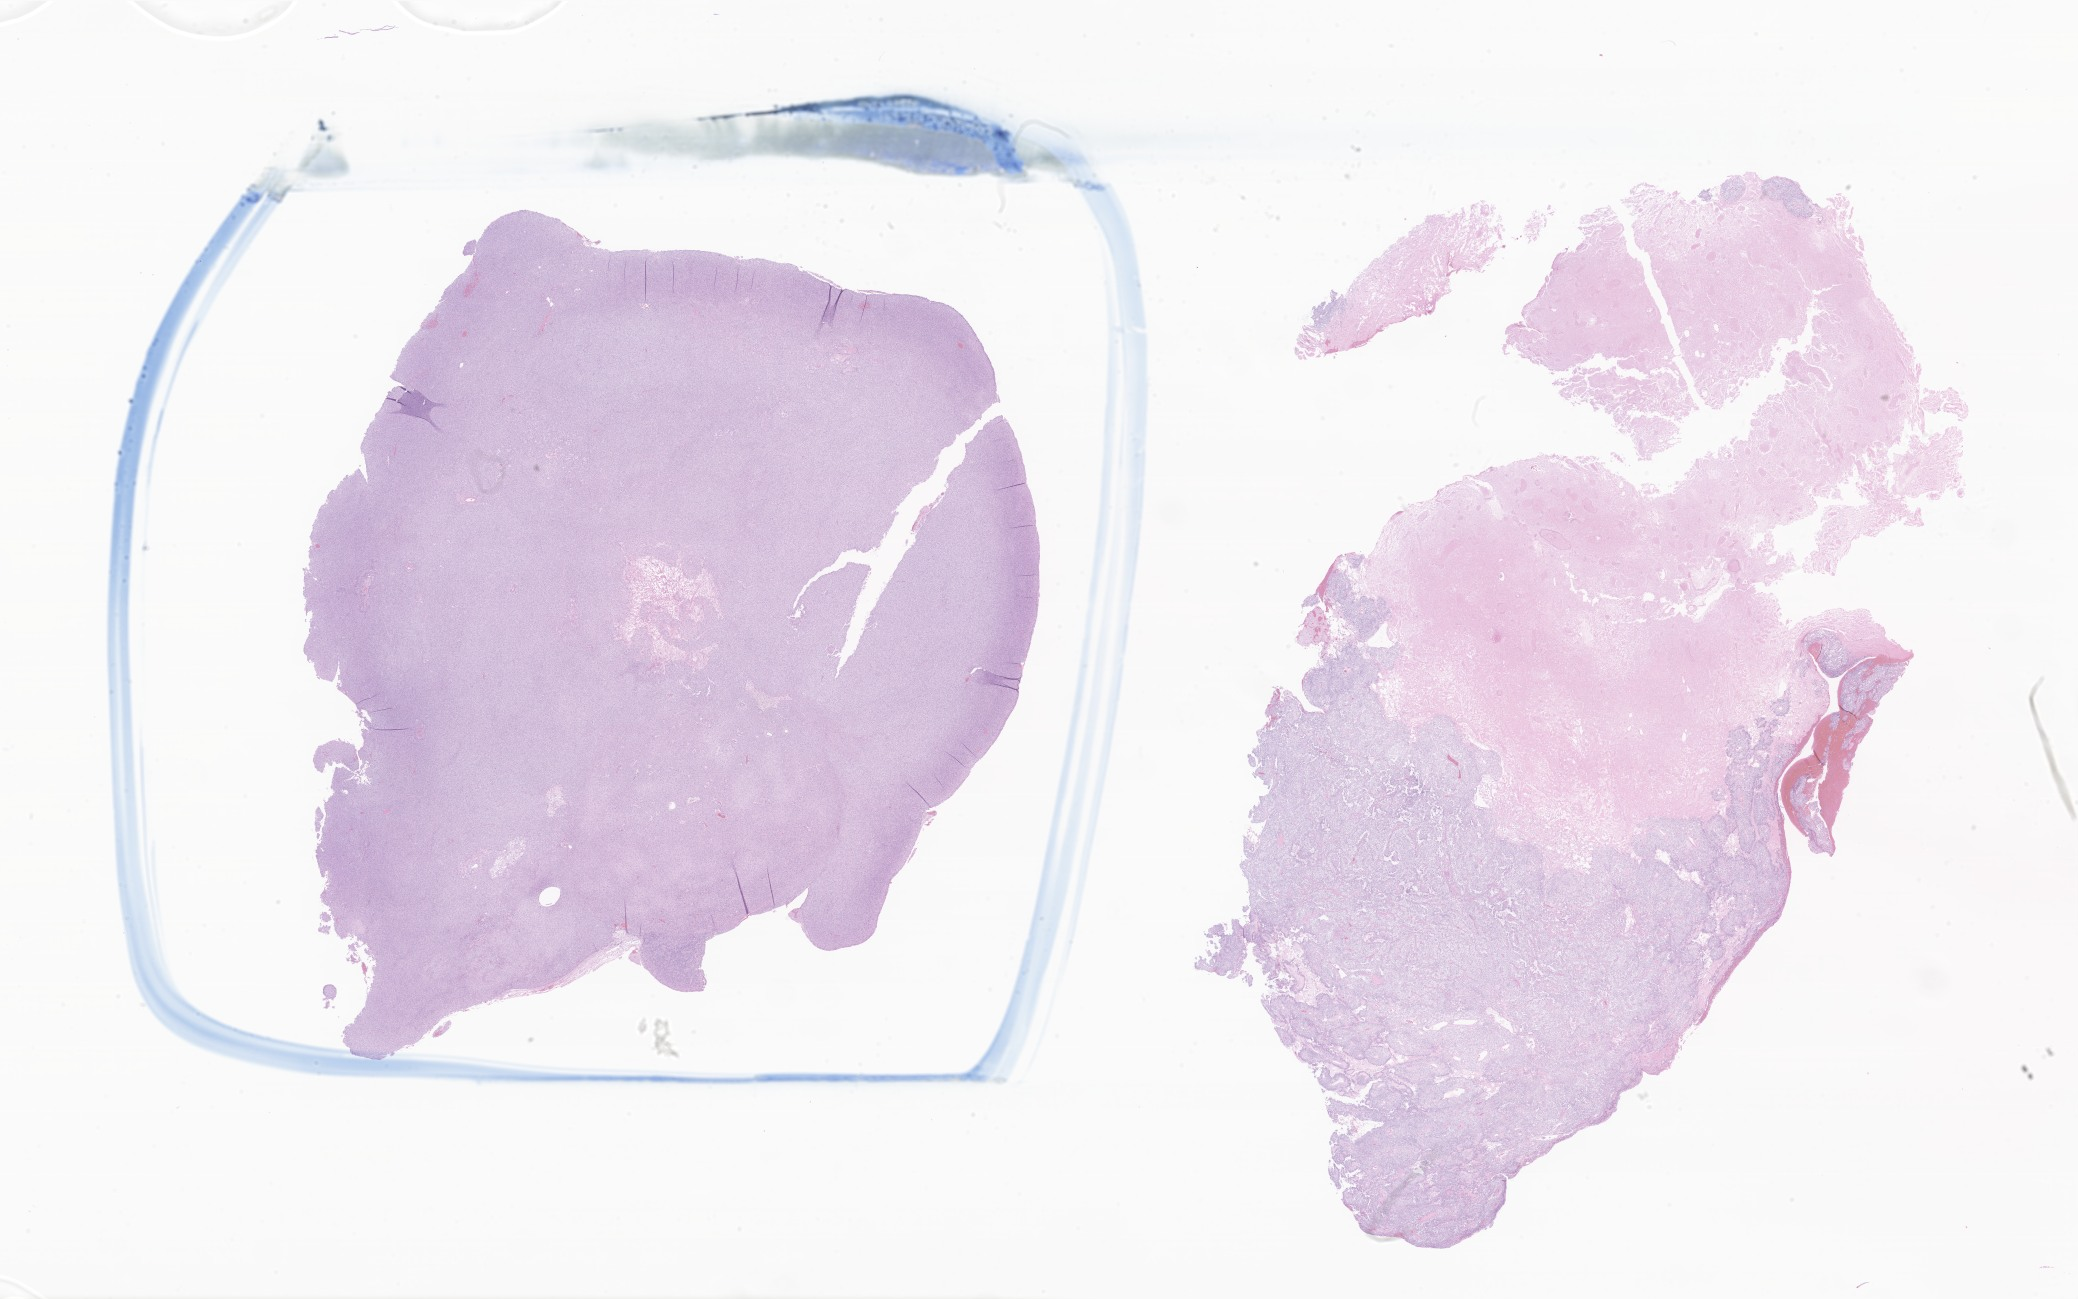
Whole-slide image, H&E stain of tumor tissue from the brain, shown as a low-resolution overview of the whole scanned area (about 35.0 x 21.9 mm); formalin-fixed, paraffin-embedded (FFPE) tissue. Patient: female, age 155 months (12 years 11 months).
Recorded diagnosis: Astroblastoma.